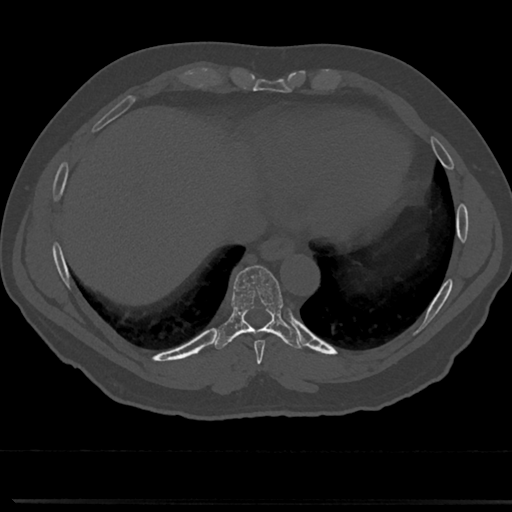
CT including the spine, one axial slice. Slice 316 of 817 in the series (ordered by position). Bone window (W 1800 / L 400 HU). 0.5 mm slice thickness. 512 × 512 image matrix, field of view 355 × 355 mm. Patient: male, 61 years. From the clinical record (not read from this slice): primary cancer: prostate.
Annotated regions visible in this slice (semi-automatically segmented with operator editing):
- T7 vertebra: bounding box <258,364,265,375> (left, top, right, bottom; pixels)
- T8 vertebra: <219,267,304,355>